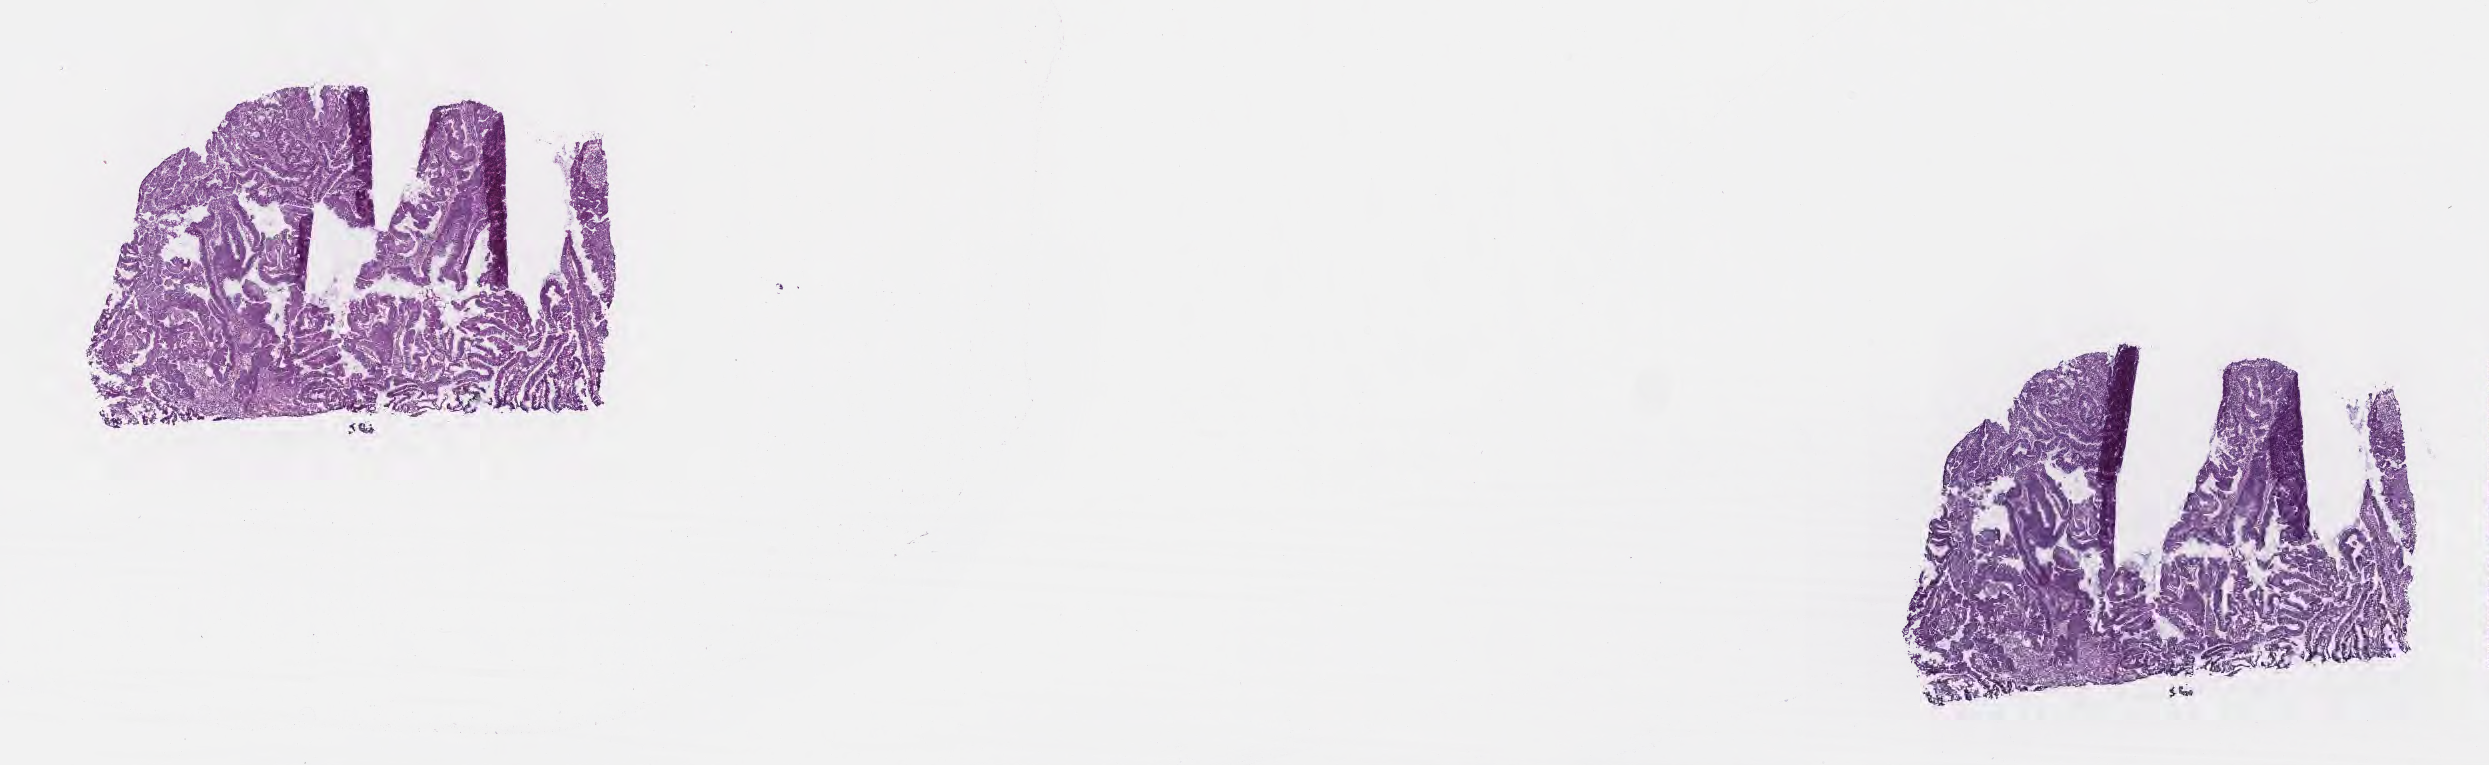
Whole-slide image, haematoxylin and eosin stain, shown as a low-resolution overview of the whole scanned area (about 20.1 x 6.2 mm); cryosection; primary tumor; anatomic site: rectum. Female patient. Tumor grade: G2 (moderately differentiated). Composition of this section per pathologist review: tumor cells 100%, tumor nuclei 70%, stromal cells 0%, necrosis 0%, normal cells 0%. Infiltration values recorded for this section: lymphocyte infiltration 0%, monocyte infiltration 0%, neutrophil infiltration 0%.
Diagnosis: Adenocarcinoma, NOS. AJCC pathologic stage: Stage I.